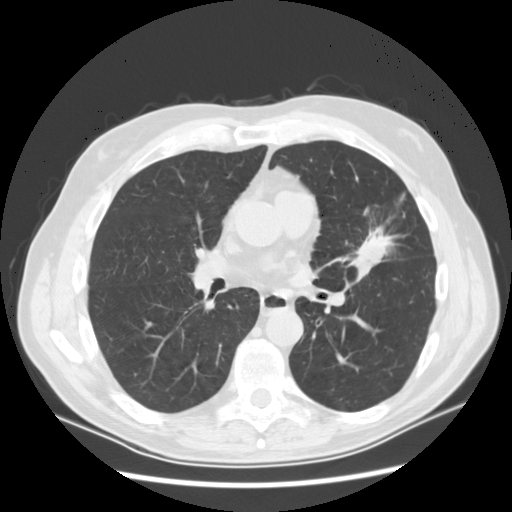
Axial slice from a low-dose chest CT screening exam. Baseline screening round. Lung window (W 1500 / L -600 HU). 120 kVp. Slice 63 of 132 in the series. Male, age 65 years at enrolment. Current smoker at enrolment.
• Expert reader's lesion annotation, box from (x=347, y=204) to (x=414, y=274) px.
• The exam's reader record, not a measurement of the box and not confirmed to be the same lesion: non-calcified nodule or mass ≥4 mm, left upper lobe, 37 × 27 mm, spiculated (stellate) margins, soft tissue attenuation.
• Official screen result: positive, change unspecified: nodule(s) >= 4 mm or enlarging nodule(s), mass(es), or other non-specific abnormalities suspicious for lung cancer.
• Lung cancer was diagnosed 56 days after this screen: non-small cell carcinoma, poorly differentiated (G3), stage IA (AJCC 6th edition).